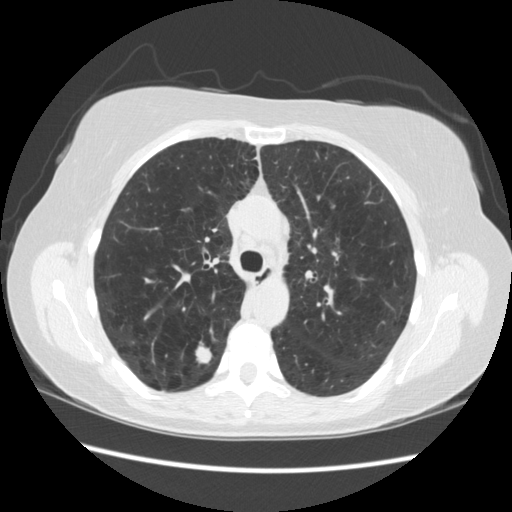
Low-dose screening chest CT, axial slice. Third screening round (two years after baseline). Lung window (W 1500 / L -600 HU). 2.5 mm slice thickness. Slice 76 of 235 in the series. Female participant, aged 55 years at enrolment. Current smoker at enrolment.
Expert-annotated lung lesion, bounding box [x1, y1, x2, y2] px = [179, 330, 228, 375]. The exam's reader record, not a measurement of the box and not confirmed to be the same lesion: non-calcified nodule or mass ≥4 mm, right upper lobe, 11 × 11 mm, poorly defined margins, soft tissue attenuation, pre-existing on the prior screen: no. Official screen result: positive, other. Later outcome: lung cancer diagnosed 96 days after this screen — small cell carcinoma, NOS, right upper lobe.